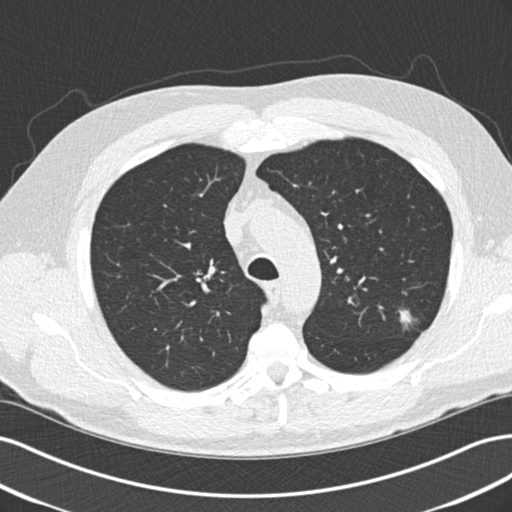
Low-dose screening chest CT, one axial slice; position 159 of 209 along the scan axis; reconstruction kernel B30f; 120 kVp; lung window (W 1500 / L -600 HU); 2 mm slice thickness; 512 × 512 image matrix, field of view 360 × 360 mm.
Outlined on this slice (manually delineated by an expert):
- lesion 1 (tumor, upper lobe of left lung): bounding box <399,310,412,326> (left, top, right, bottom; pixels)